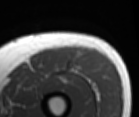
MRI of an extremity soft-tissue mass, one axial slice. Slice 35 of 86 in the series (ordered by position). MR volume resampled by the dataset authors to the PET/CT grid (not the native acquisition matrix). 3.27 mm slice thickness. 139 × 117 image matrix. Male patient. From the clinical record (not read from this slice): histological type: extraskeletal osteosarcoma; grade: high; site of the primary tumour: thigh.
Outlined on this slice (expert contour drawn on MRI and transferred to this co-registered scan by the dataset authors):
- gross tumour volume (mass): box from (x=74, y=52) to (x=80, y=67) px